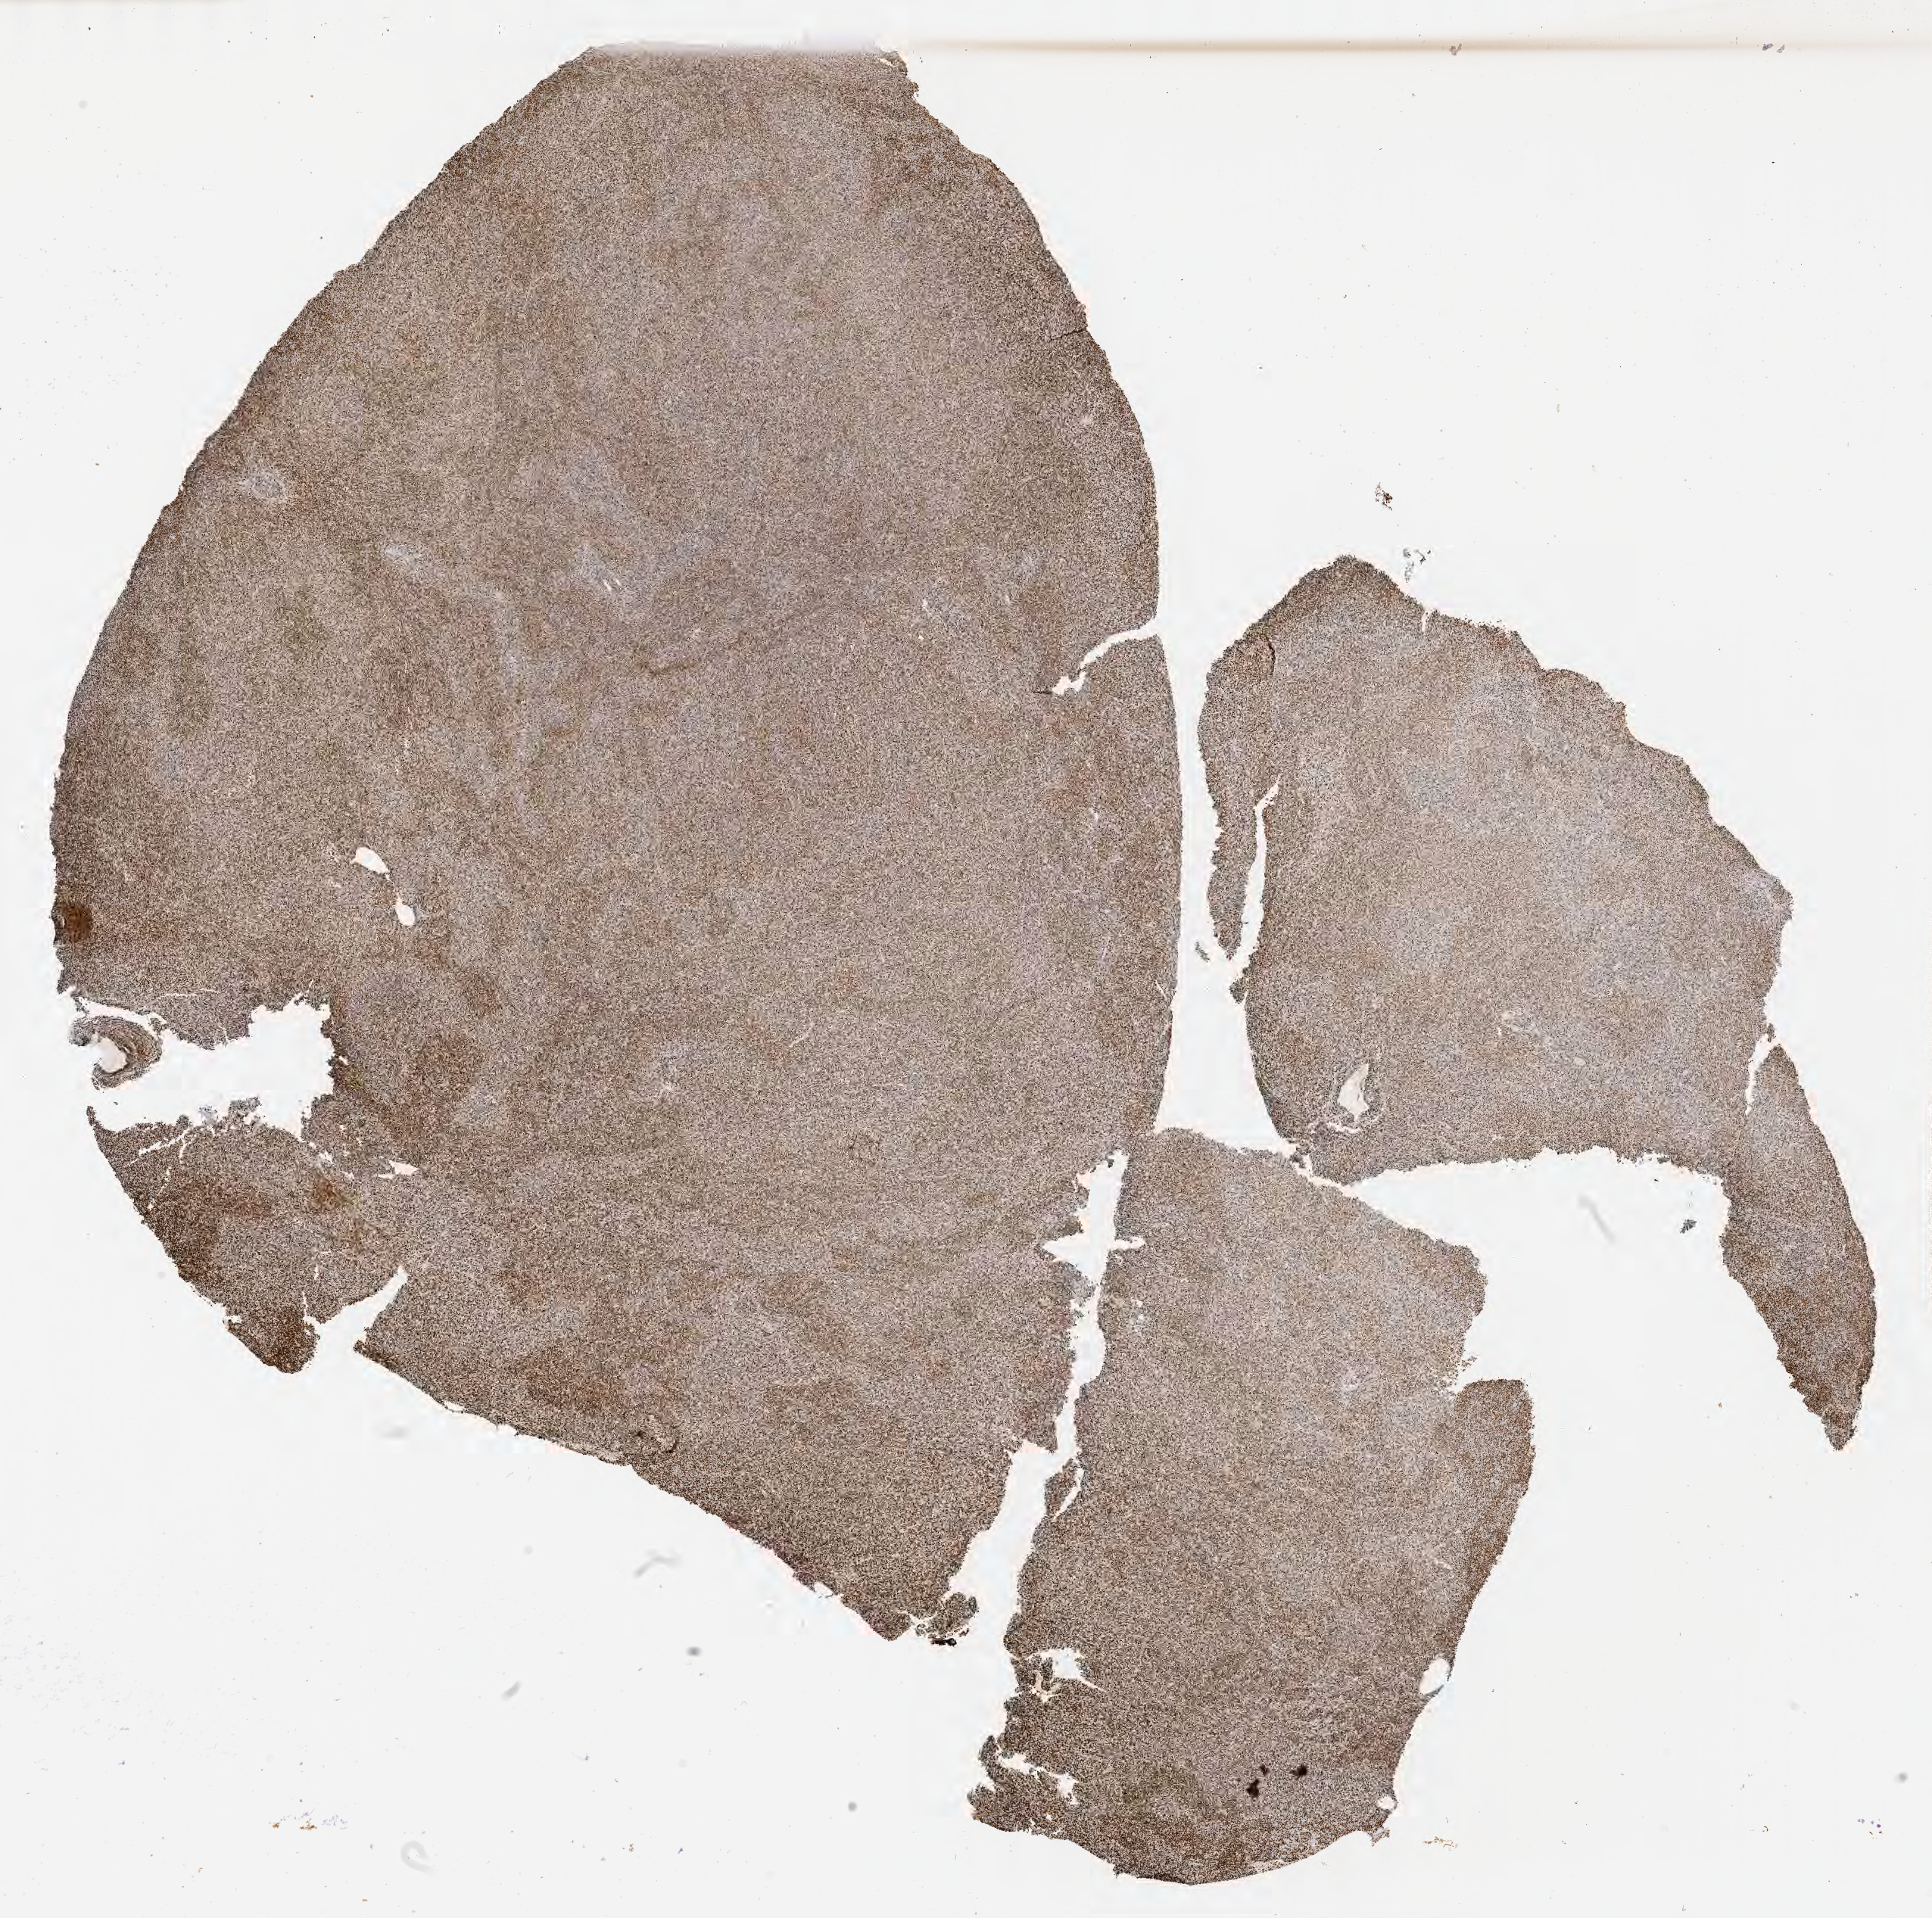
IHC for Ki-67, whole-slide image — whole scanned area (about 20.6 x 20.5 mm) shown as a low-resolution overview, tumor tissue, anatomic site: liver. Patient female; age 46 years.
Diagnosis: Diffuse large B-cell lymphoma, NOS.